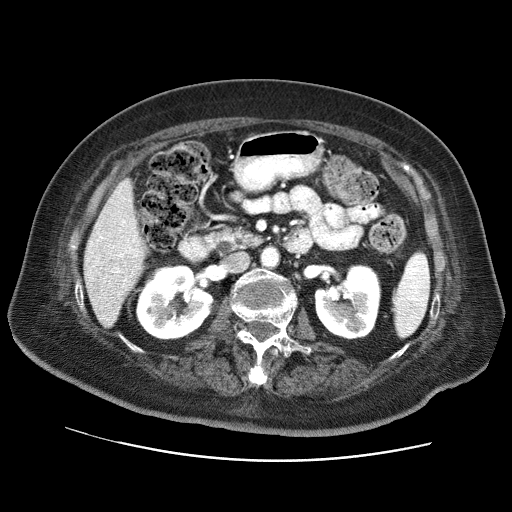
Contrast-enhanced abdominal CT (liver protocol), one axial slice. Position 25 of 73 along the scan axis. Reconstruction kernel STANDARD. 120 kVp. Soft-tissue window (W 400 / L 40 HU). 512 × 512 image matrix, field of view 380 × 380 mm. From the clinical record (not read from this slice): diagnosis: hepatocellular carcinoma (patient treated with transarterial chemoembolisation; whether this scan precedes or follows treatment is not stated here); TNM stage (as recorded): Stage-I; Child-Pugh class: A; tumour nodularity: uninodular.
Structures marked on this image (semi-automatically segmented with operator editing):
- liver parenchyma outside the tumour (the mass and vessels are separate outlines, so this box may not span the whole liver): bounding box (x1, y1, x2, y2) in pixels: (84, 178, 144, 326)
- liver vessels: (90, 198, 138, 282)